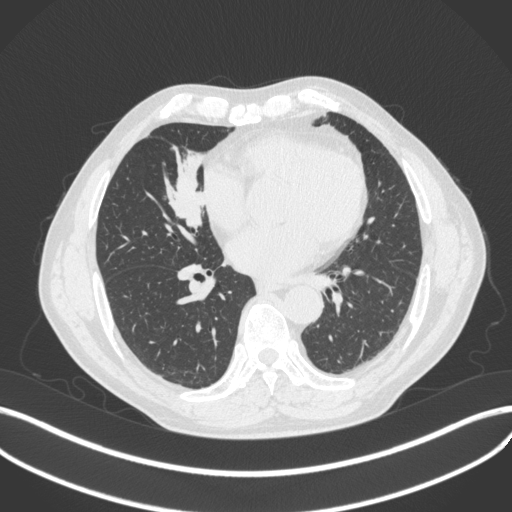
Chest CT, one axial slice; position 172 of 429 along the scan axis; 120 kVp; lung window (W 1500 / L -600 HU); 1 mm slice thickness; 512 × 512 image matrix. Patient: male, 61 years. From the clinical record (not read from this slice): clinical TNM (as recorded): T2b N1 M0.
Outlined on this slice (bounding box drawn by a radiologist):
- lung tumour (recorded histology: squamous cell carcinoma): box from (x=155, y=141) to (x=210, y=233) px